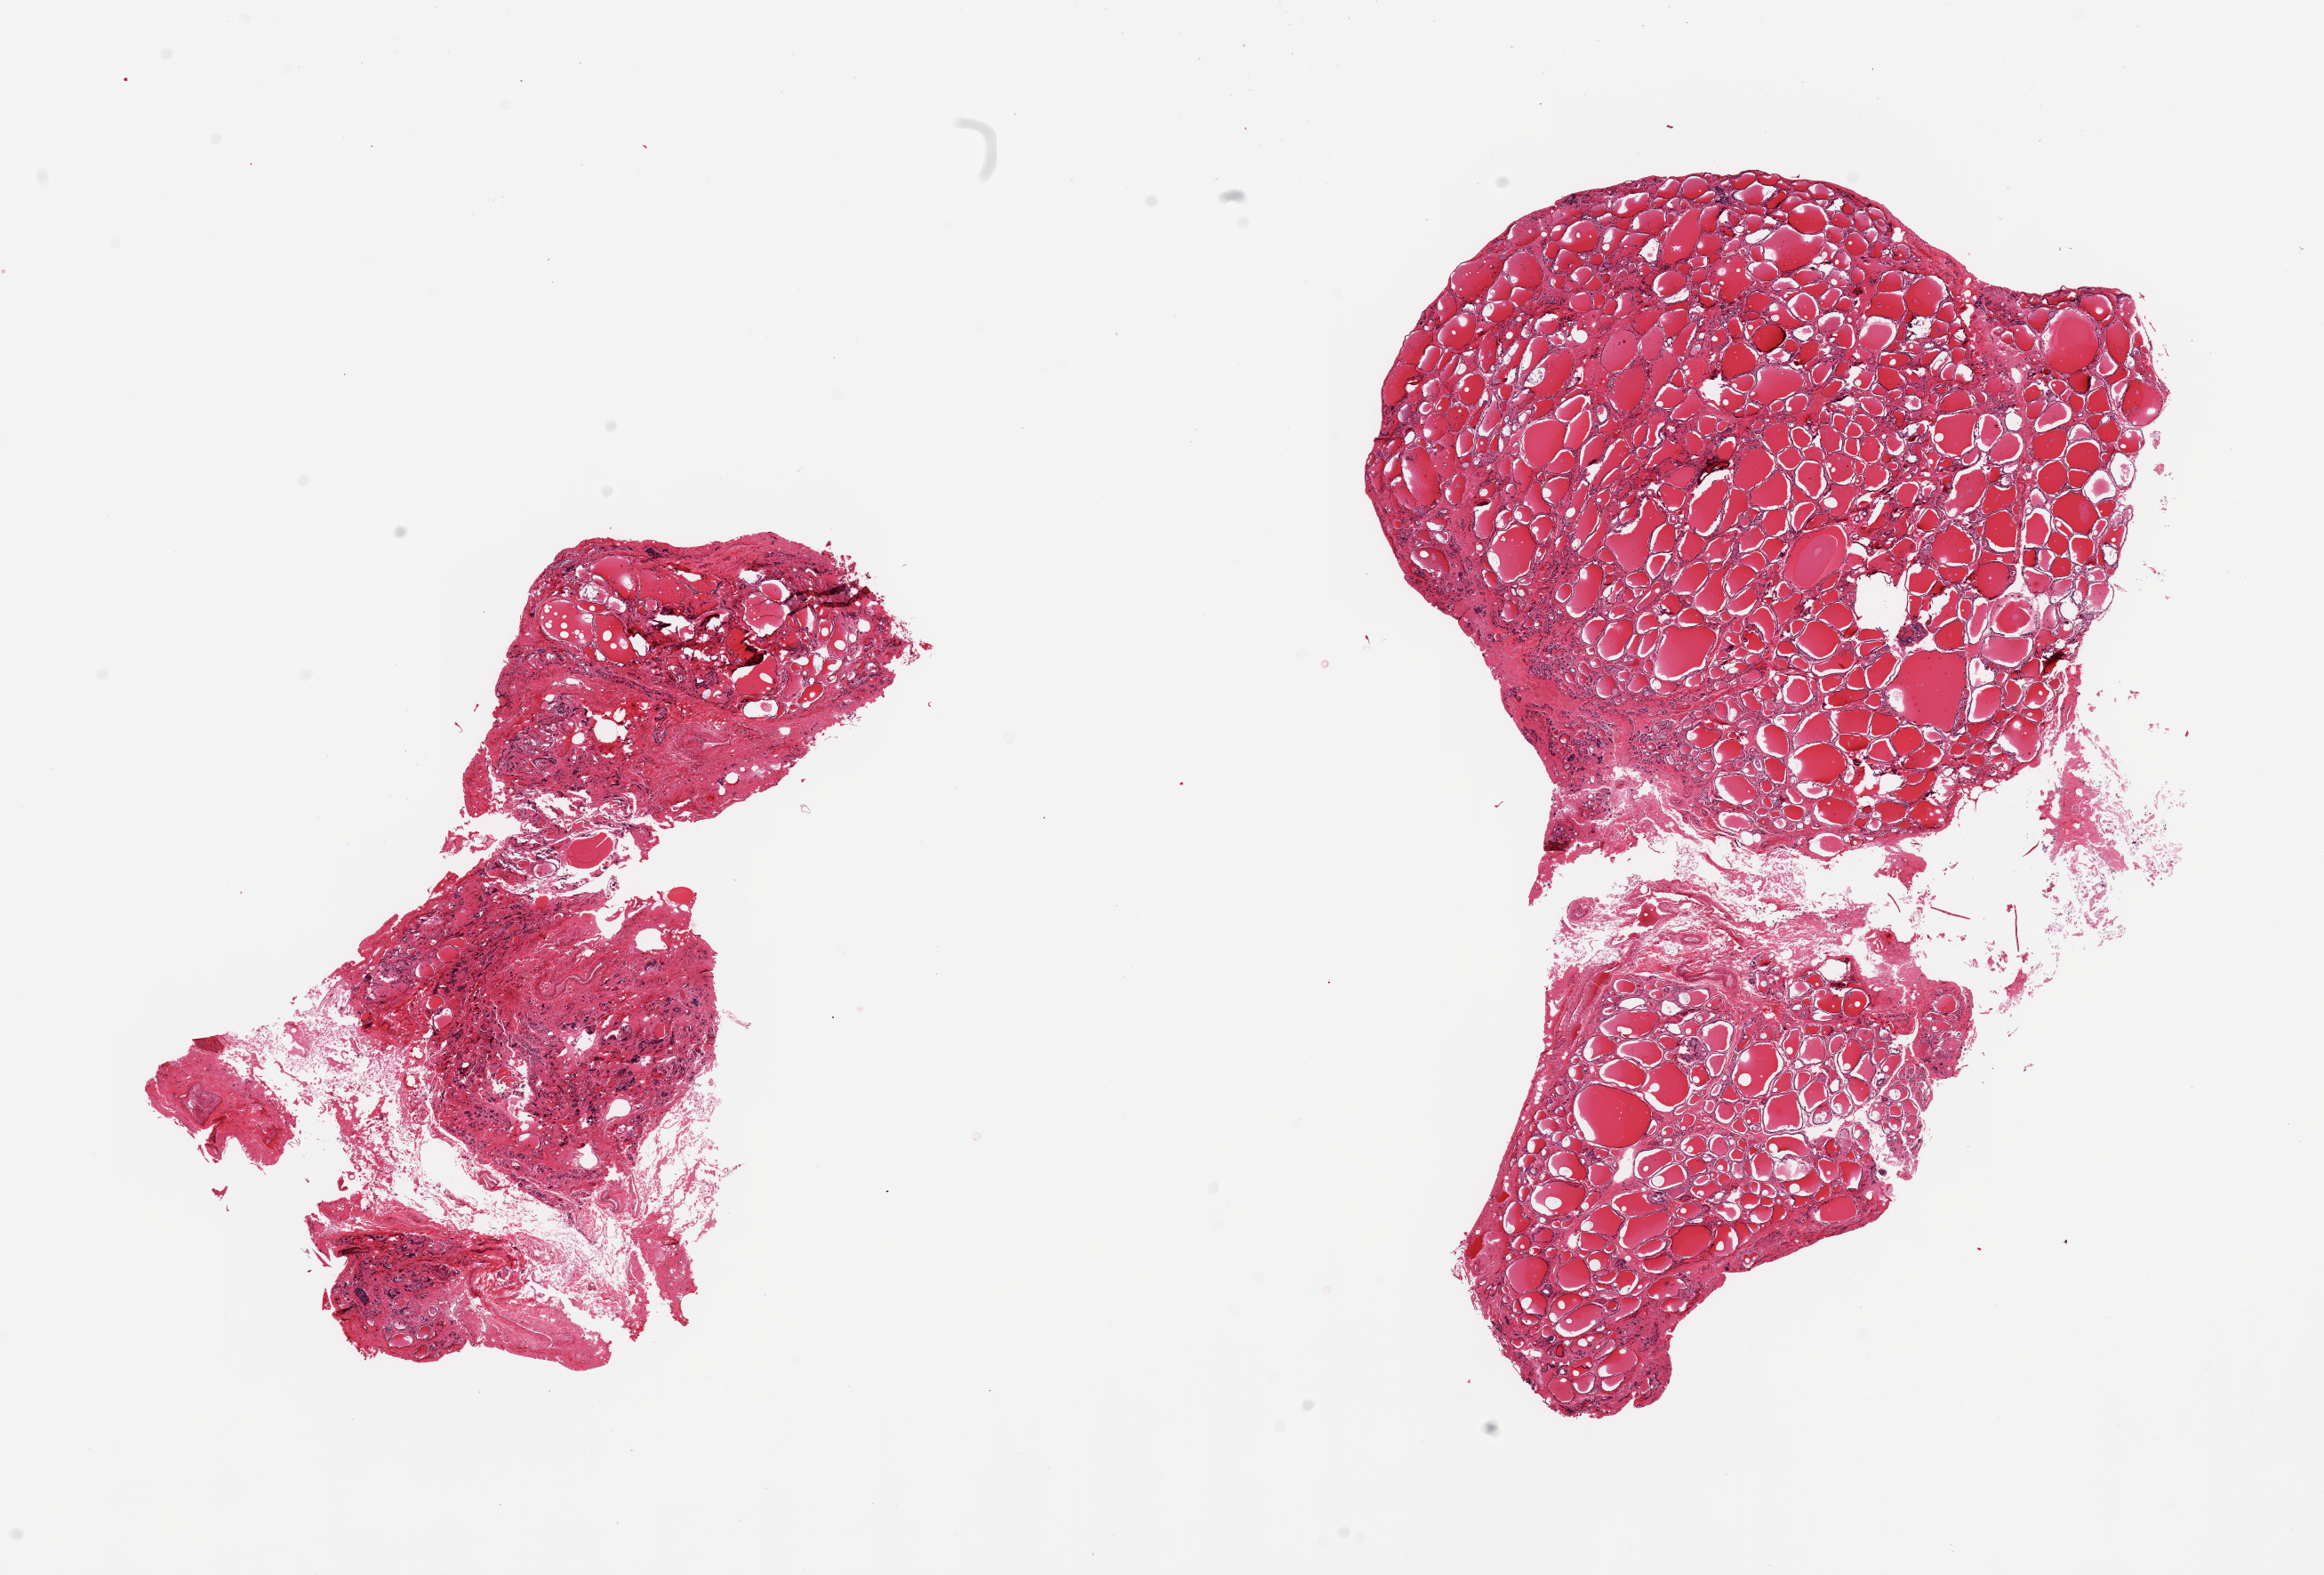
Digitized haematoxylin and eosin-stained section, low-resolution overview of the scanned area, about 20.7 x 14.0 mm, PAXgene-fixed paraffin-embedded (PFPE) section, target tissue: thyroid, donor tissue sample. Donor: female.
- reviewer comment on this tissue sample: 2 pieces; nodular hyperplasia with regressive changes